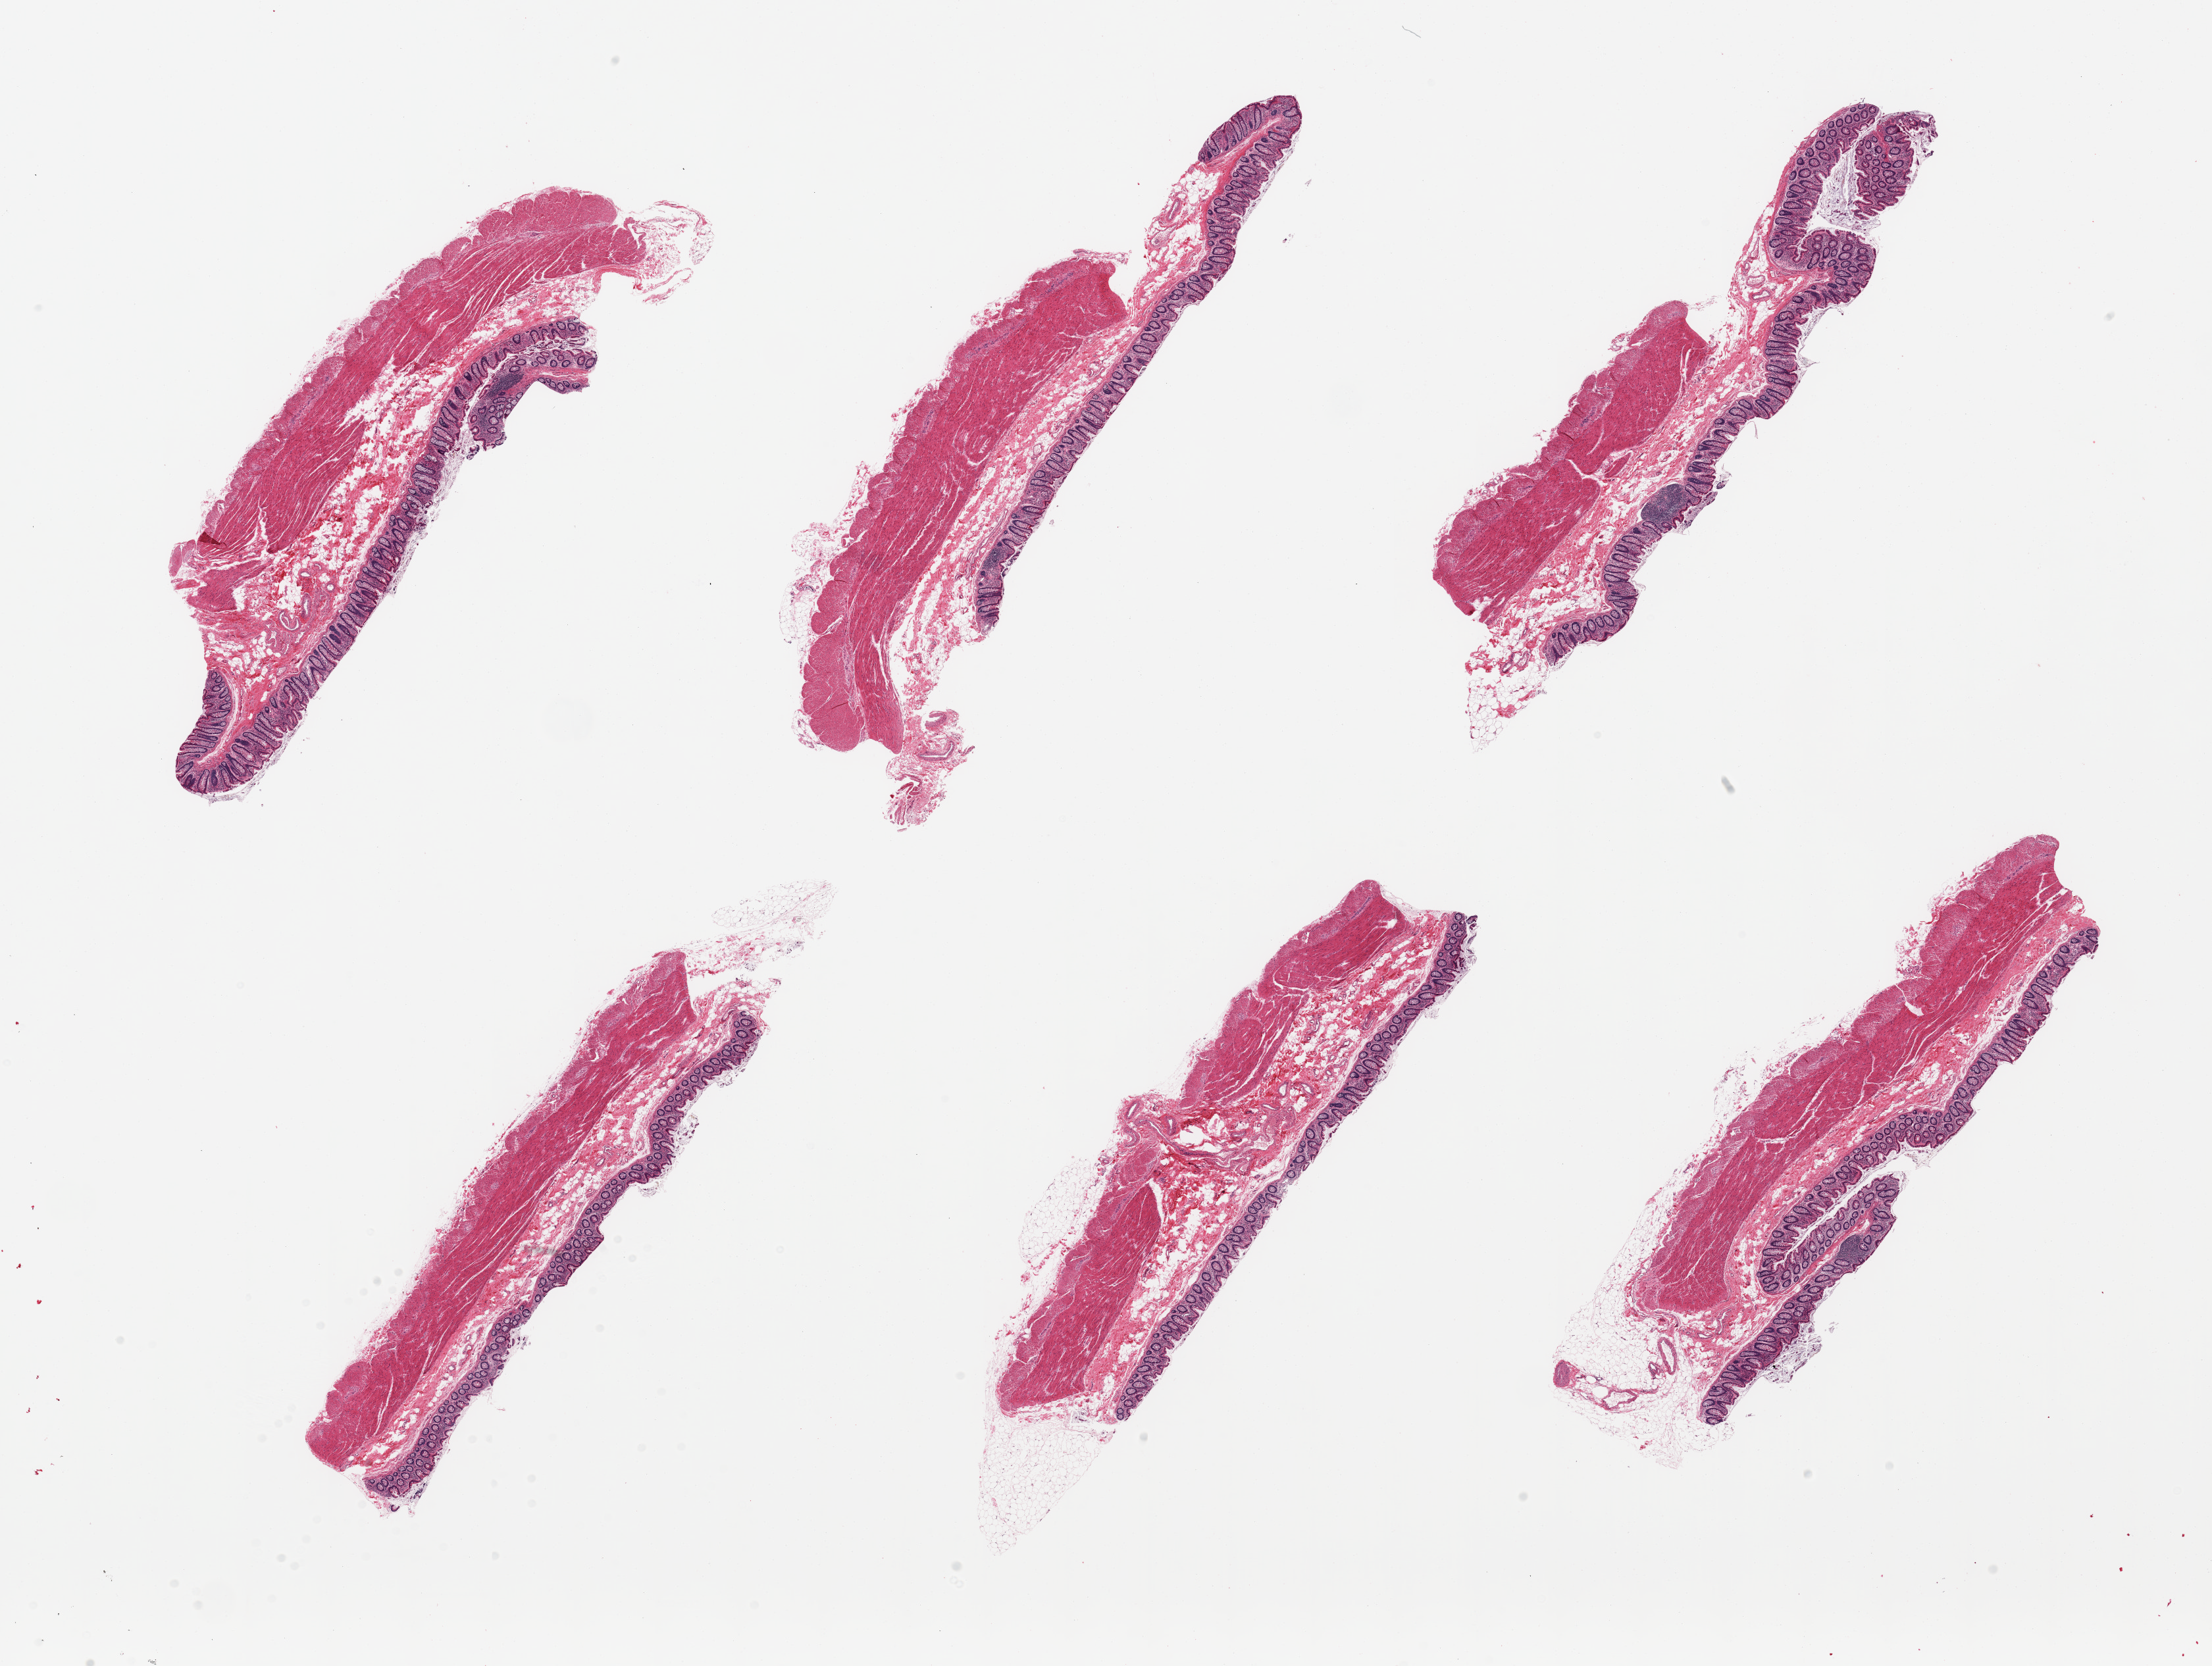
H&E whole-slide image, a low-resolution overview of the entire scanned area, about 26.6 x 20.0 mm (acquisition: 20x scan); PAXgene-fixed paraffin-embedded (PFPE) section; target tissue: transverse colon; tissue donor sample.
- reviewer comment on this tissue sample: 6 pieces, mucosa up to ~0.4mm, ~15-20% thickness